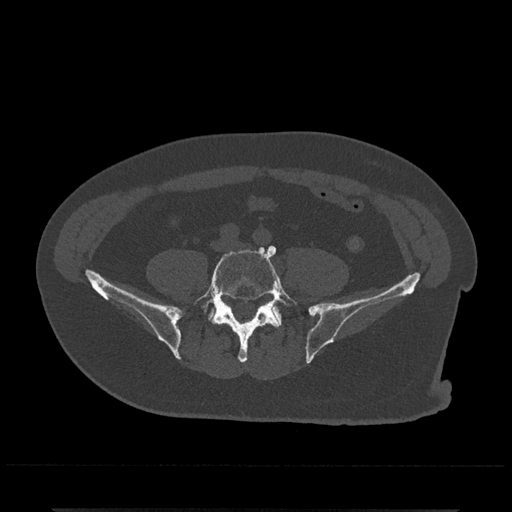
CT including the spine, one axial slice; position 83 of 797 along the scan axis; reconstruction kernel Br40s/3; bone window (W 1800 / L 400 HU); 512 × 512 image matrix. Male patient, age 67 years. Case-level facts recorded for this patient, not image findings: primary cancer: prostate.
Annotated regions visible in this slice (semi-automatically segmented with operator editing):
- L5 vertebra: box from (x=193, y=245) to (x=298, y=363) px